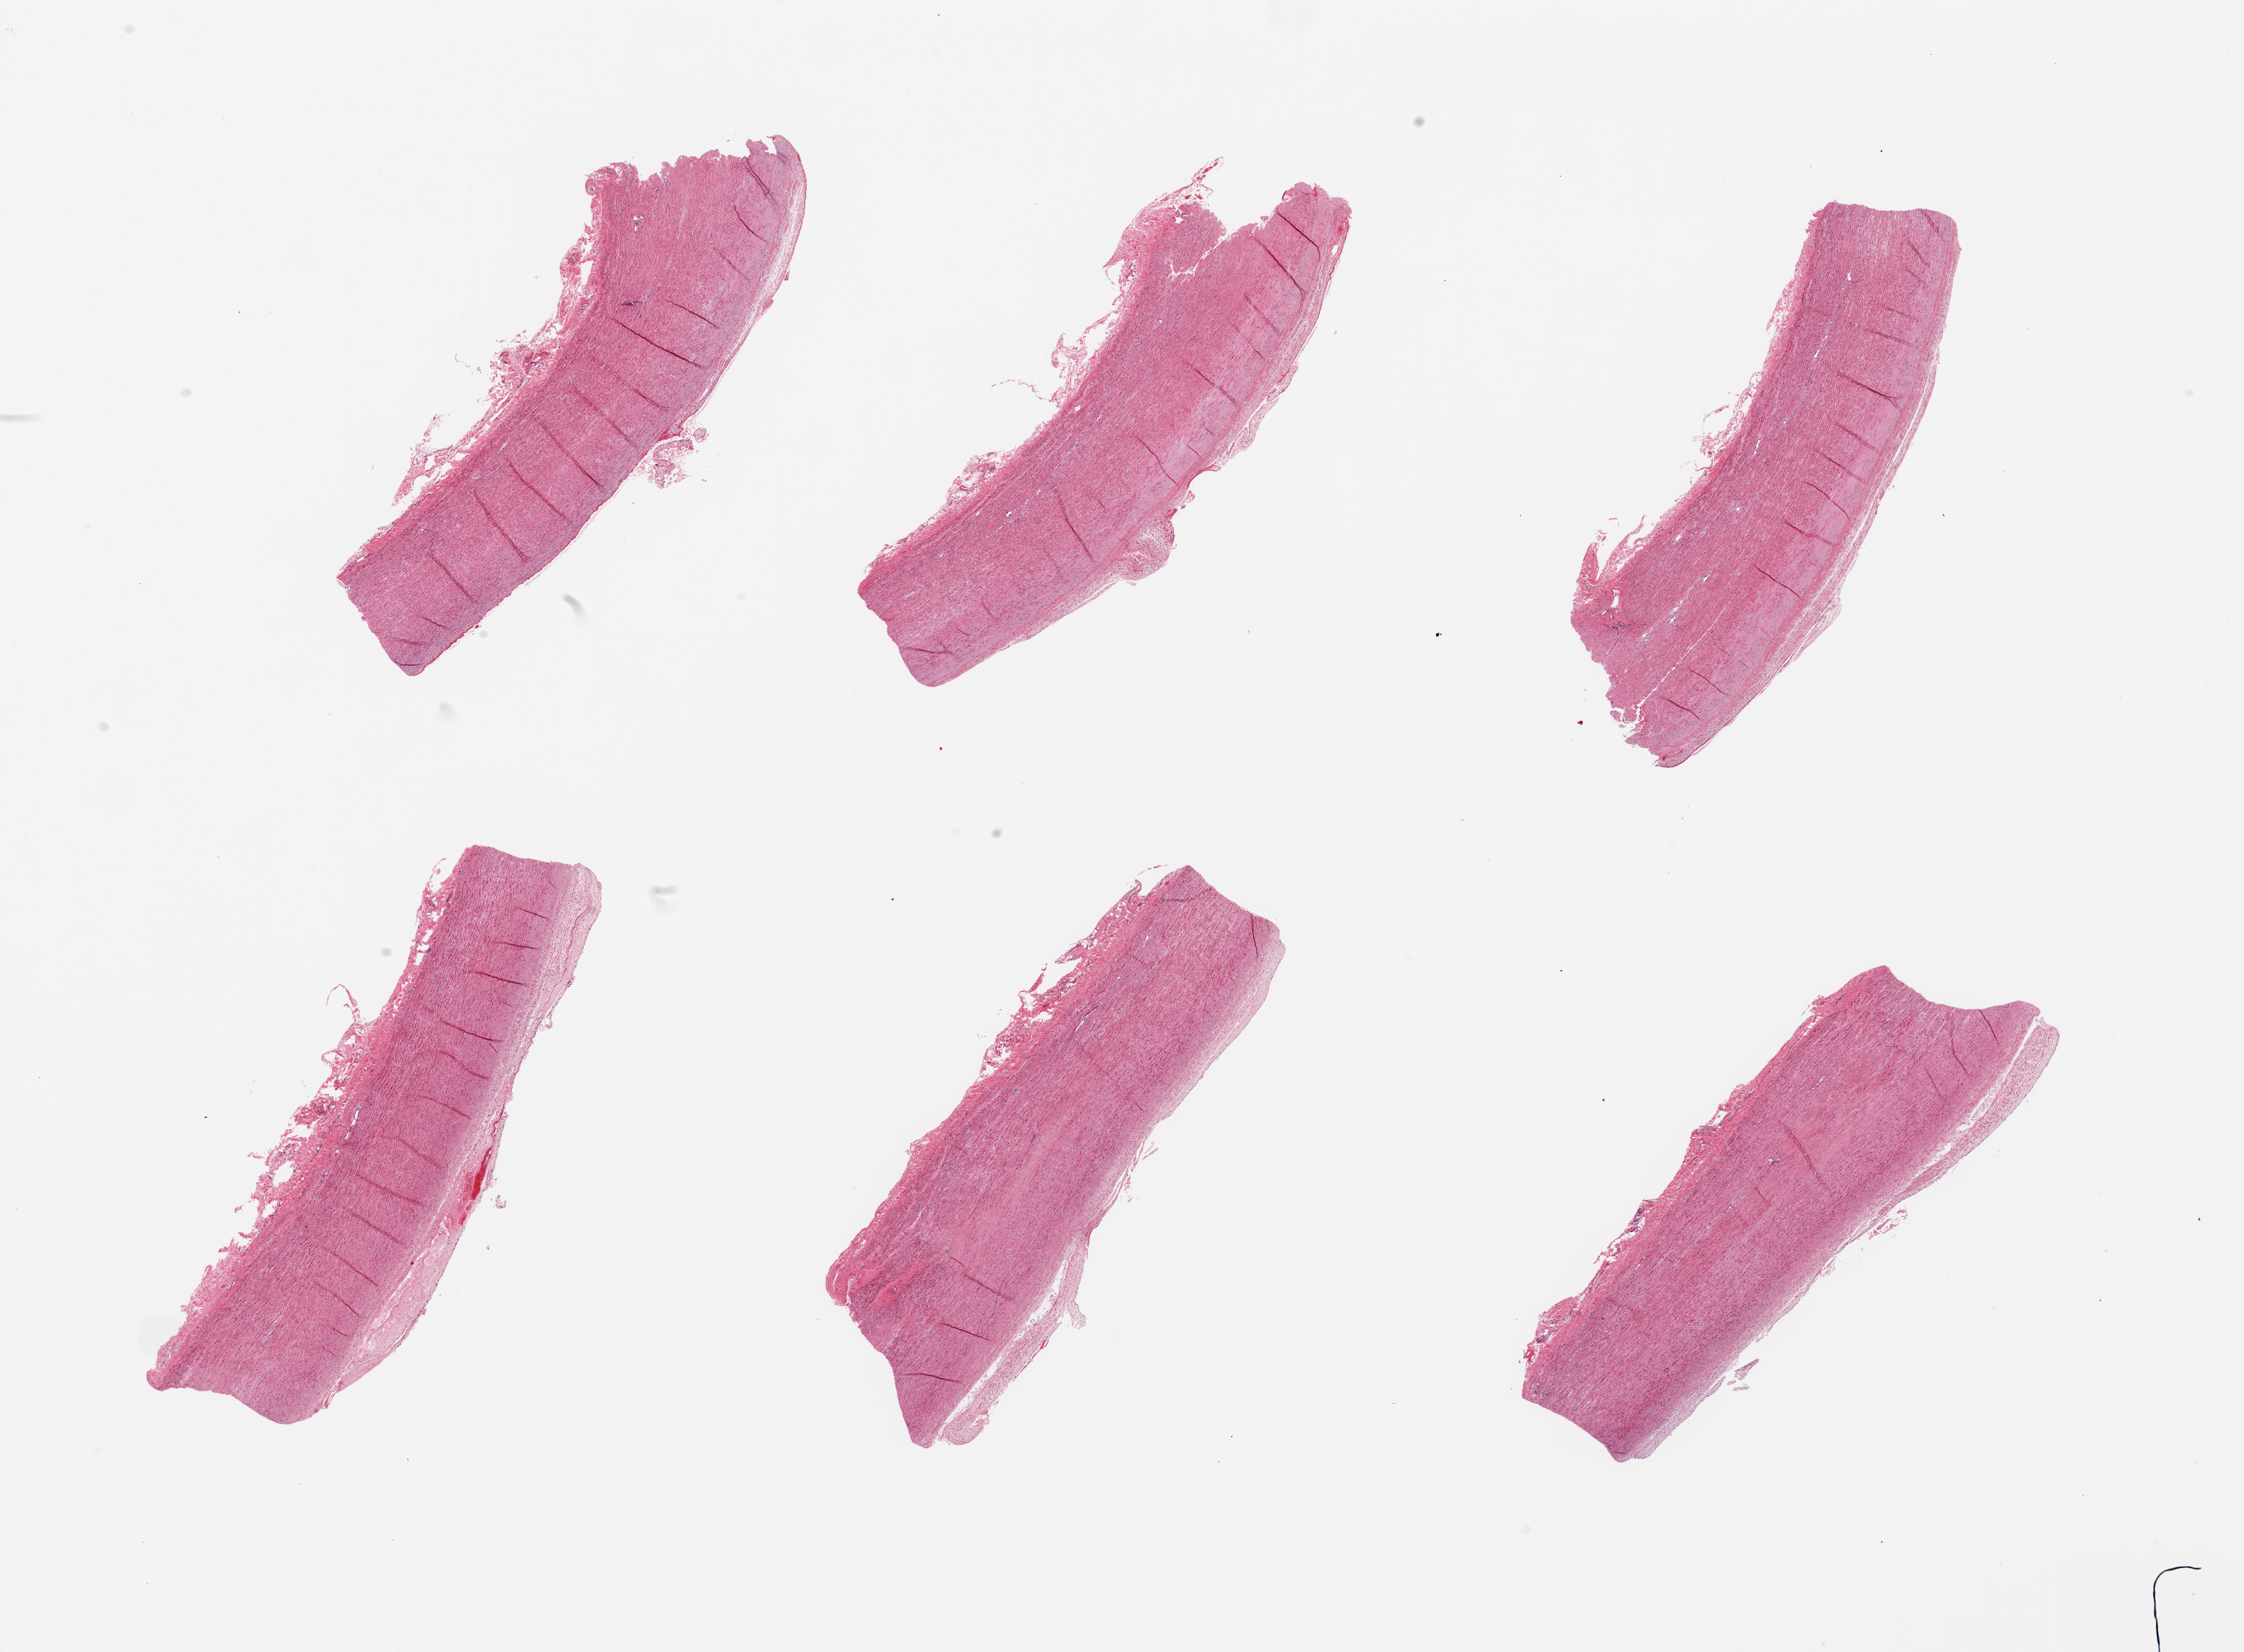
Digitized H&E-stained section, a low-resolution overview of the entire scanned area, about 25.6 x 18.8 mm; PAXgene-fixed paraffin-embedded (PFPE) section; sampled site (target tissue): aorta; donor tissue sample. Donor sex: male.
Reviewer comment on this tissue sample: 6 pieces, atherosis up to ~0.5mm.